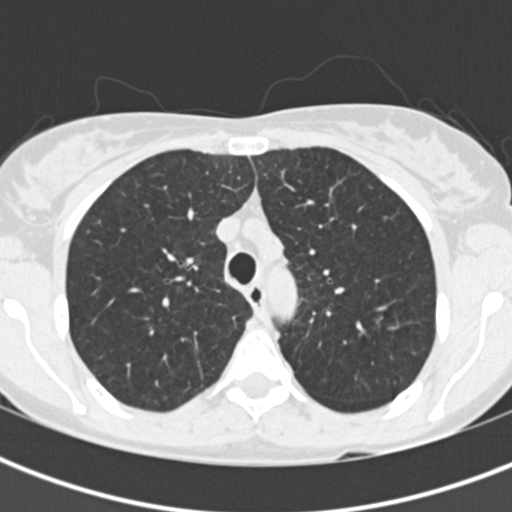
Chest CT (low-dose screening protocol), one axial image; baseline annual screen; lung window (W 1500 / L -600 HU); slice 51 of 199 in the series. Female, age 56 years at enrolment. Current smoker at enrolment.
Expert reader's lesion annotation, bounding box [x1, y1, x2, y2] px = [366, 305, 399, 344]. Reader record for this screening exam (exam-level; its link to the box is not recorded): non-calcified nodule or mass ≥4 mm, right upper lobe, 6 × 5 mm, poorly defined margins, ground glass attenuation. Note: the box lies in the patient's left hemithorax on this image, whereas the reader's record names the right lung; they may be different findings.